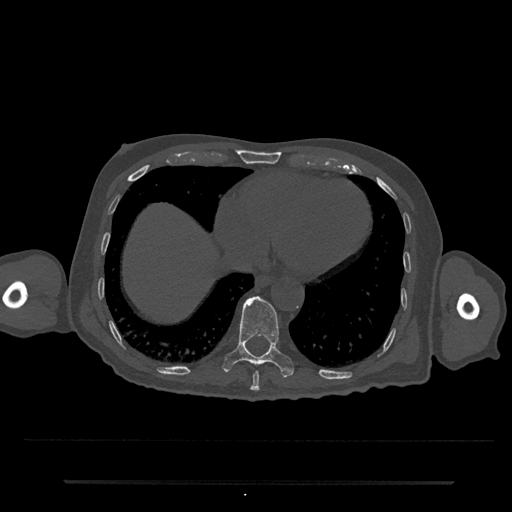
CT including the spine, one axial slice. Position 320 of 797 along the scan axis. Reconstruction kernel Br40s/3. Bone window (W 1800 / L 400 HU). 0.5 mm slice thickness. 512 × 512 image matrix, field of view 427 × 427 mm. Patient: male, 74 years. Case-level facts recorded for this patient, not image findings: primary cancer: prostate.
Annotated regions visible in this slice (semi-automatically segmented with operator editing):
- T10 vertebra: bounding box [x1, y1, x2, y2] px = [222, 296, 294, 378]
- T9 vertebra: [250, 371, 260, 392]